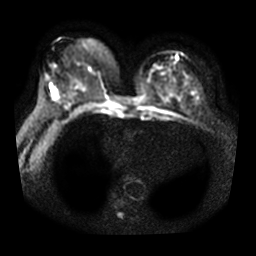
Breast MRI, one axial slice. Slice 17 of 36 in the series (ordered by position). Diffusion-weighted series; image 2 of 4 stored at this slice position (different b-values; order by instance number). 3 T. 5 mm slice thickness. 256 × 256 image matrix, field of view 340 × 340 mm. Female patient.
Structures marked on this image (manually delineated by an expert):
- tumour on diffusion-weighted imaging: box from (x=52, y=89) to (x=56, y=94) px